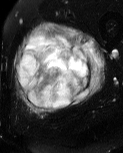
MRI of an extremity soft-tissue mass, one axial slice; position 21 of 60 along the scan axis; T2-weighted fat-saturated; MR volume resampled by the dataset authors to the PET/CT grid (not the native acquisition matrix); 3.27 mm slice thickness; 123 × 153 image matrix, field of view 120 × 149 mm. Male patient. From the clinical record (not read from this slice): histological type: pleiomorphic liposarcoma; grade: high; site of the primary tumour: left thigh.
Structures marked on this image (expert contour drawn on MRI and transferred to this co-registered scan by the dataset authors):
- gross tumour volume including surrounding oedema: bounding box (x1, y1, x2, y2) in pixels: (15, 22, 107, 117)
- gross tumour volume (mass): (18, 33, 92, 110)